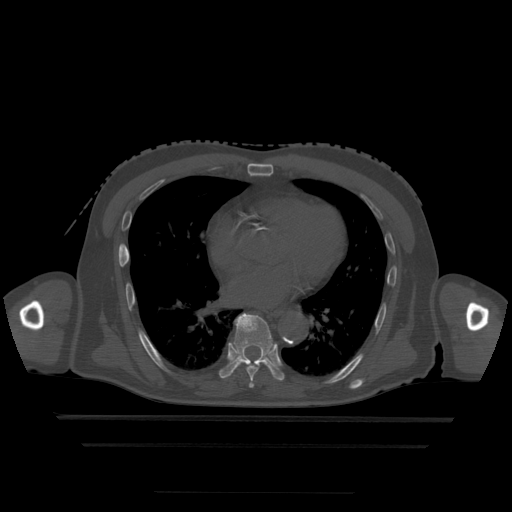
CT including the spine, one axial slice; position 288 of 522 along the scan axis; bone window (W 1800 / L 400 HU); 1.25 mm slice thickness; 512 × 512 image matrix, field of view 436 × 436 mm. Patient age 68 years. Case-level facts recorded for this patient, not image findings: primary cancer: urothelial.
Outlined on this slice (semi-automatically segmented with operator editing):
- T6 vertebra: bounding box (x1, y1, x2, y2) in pixels: (250, 381, 254, 388)
- T7 vertebra: (247, 365, 259, 382)
- T8 vertebra: (219, 314, 285, 381)